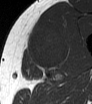
MRI of an extremity soft-tissue mass, one axial slice. Position 38 of 62 along the scan axis. MR volume resampled by the dataset authors to the PET/CT grid (not the native acquisition matrix). 3.27 mm slice thickness. 92 × 104 image matrix, field of view 90 × 102 mm. Male patient. Case-level facts recorded for this patient, not image findings: histological type: mixoid liposarcoma; grade: low; site of the primary tumour: left thigh.
Outlined on this slice (expert contour drawn on MRI and transferred to this co-registered scan by the dataset authors):
- gross tumour volume (mass): bounding box [x1, y1, x2, y2] px = [26, 26, 70, 71]